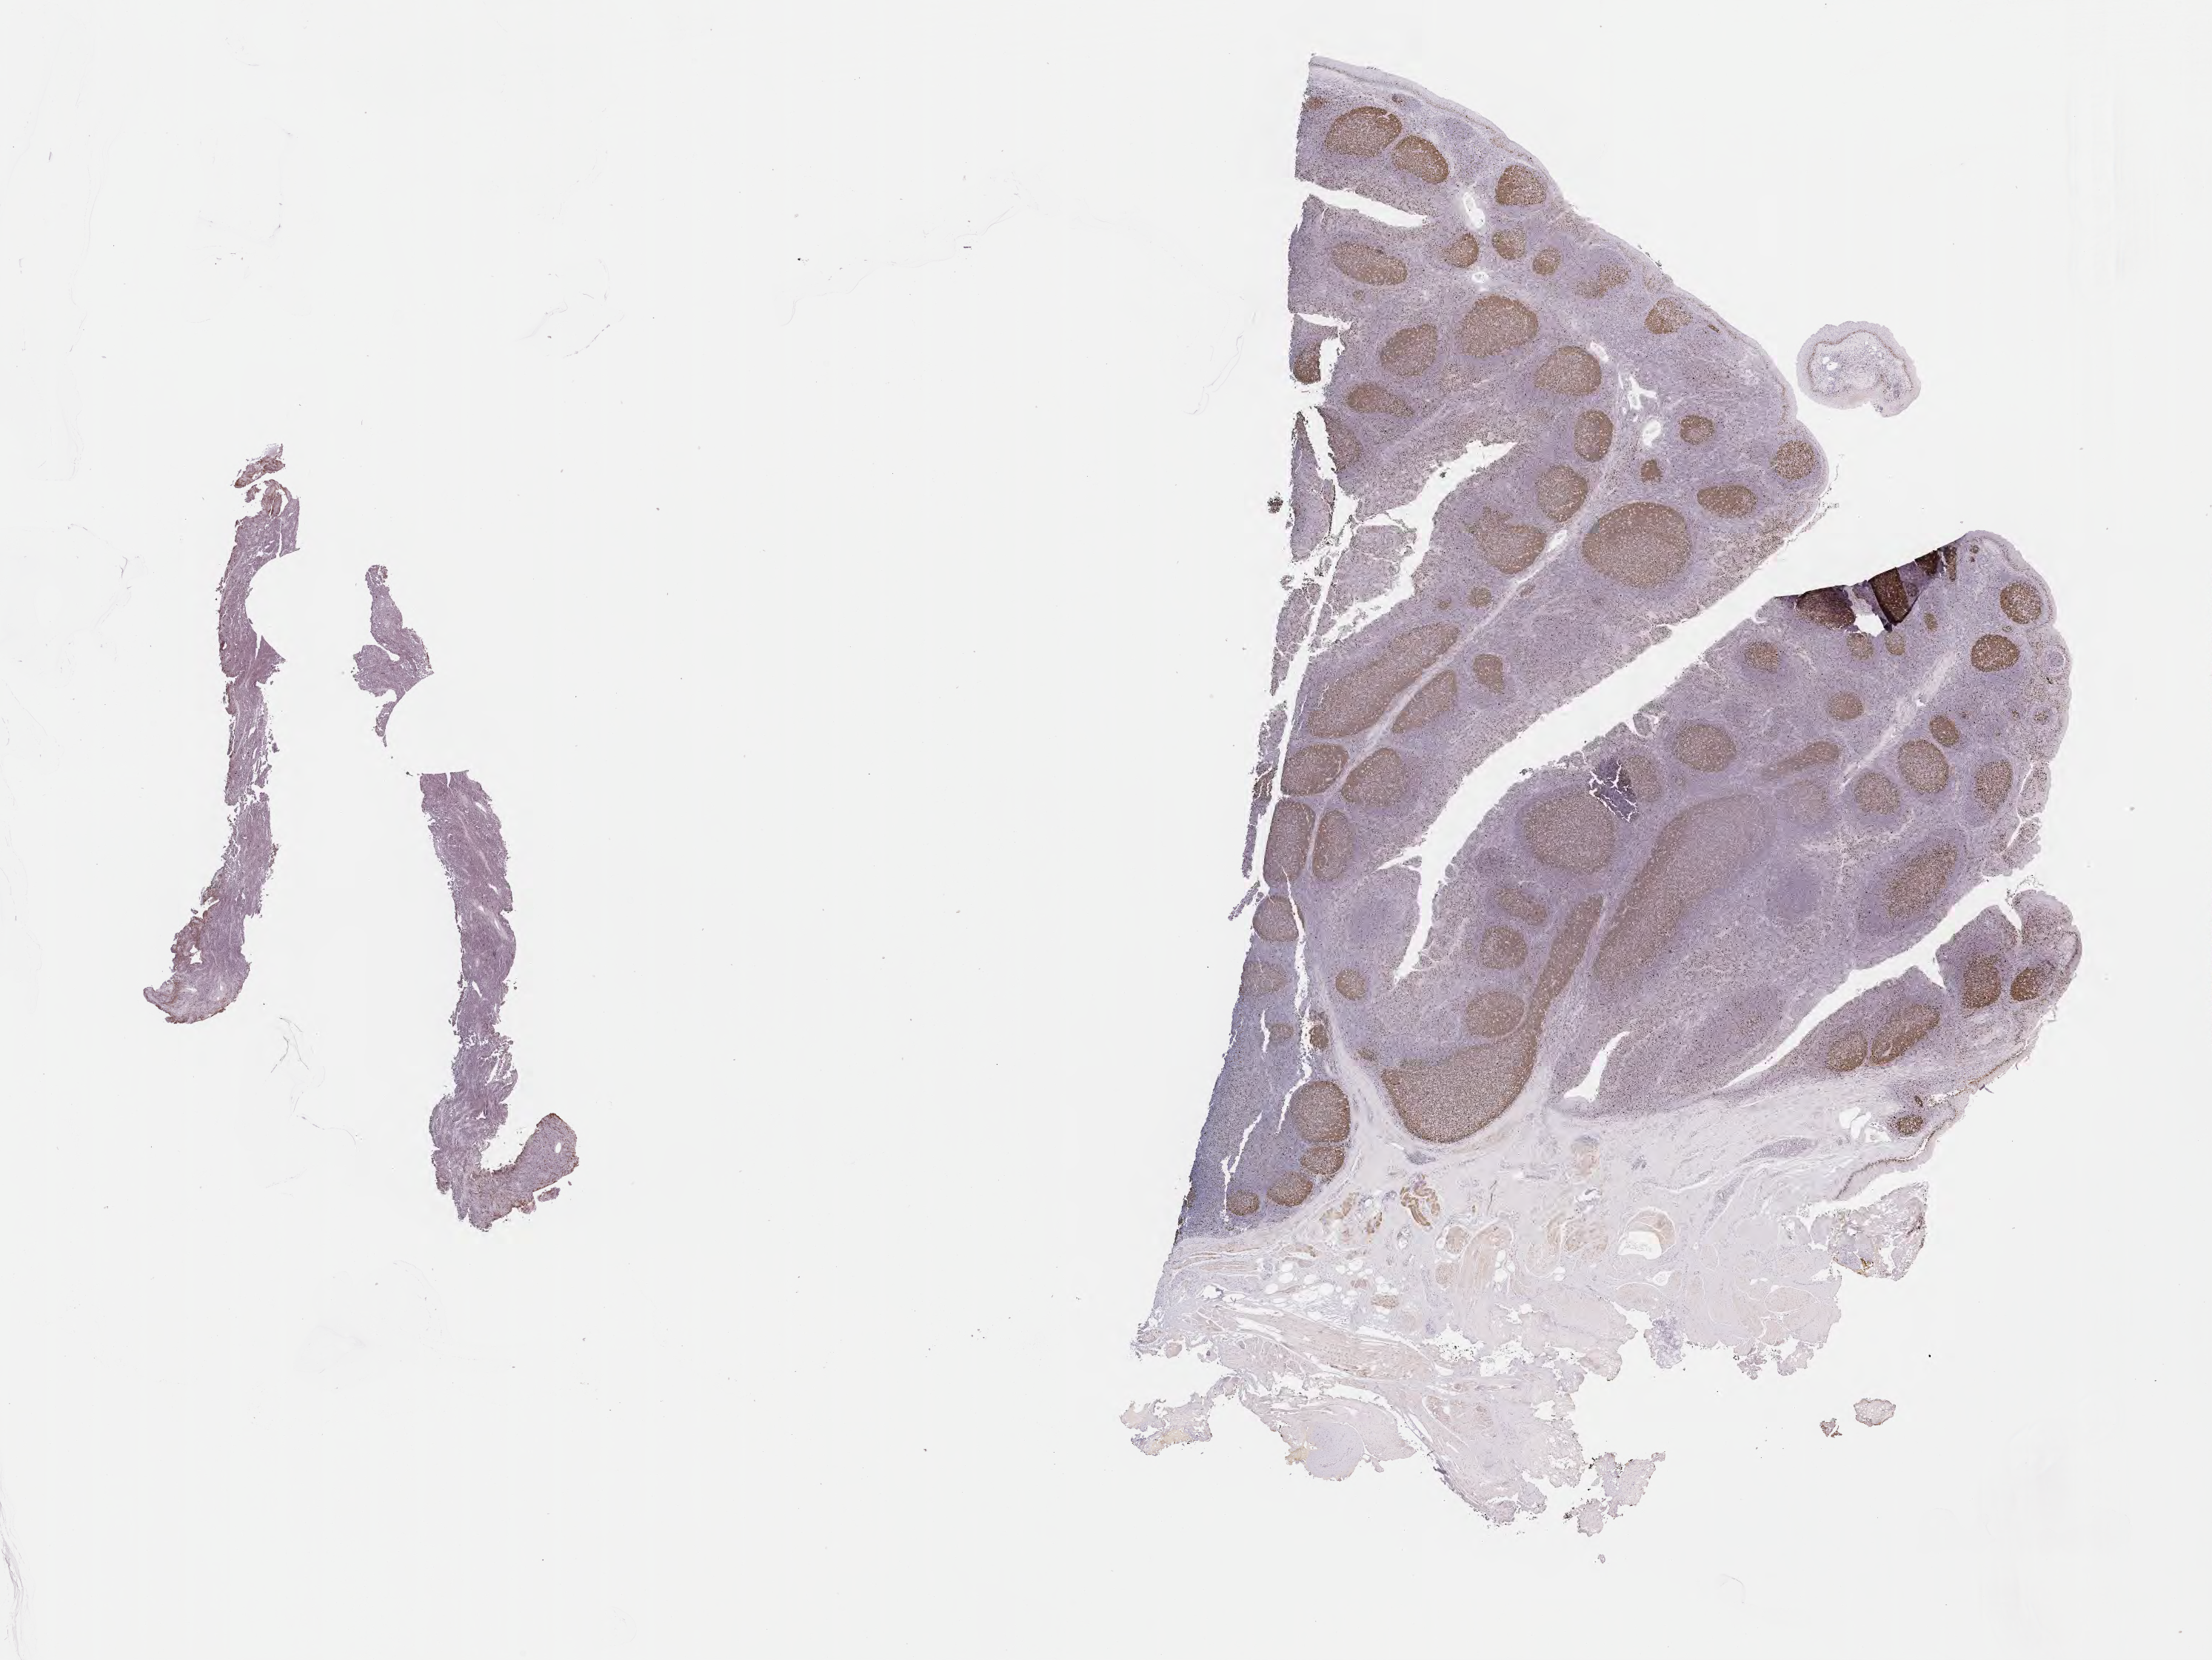
Whole-slide image, immunohistochemical stain for Ki-67 — shown as a low-resolution overview of the whole scanned area (about 24.2 x 18.1 mm), specimen: tumor tissue, site: spleen. Male patient; age at initial diagnosis 6 years.
Diagnosis: Burkitt lymphoma, NOS.